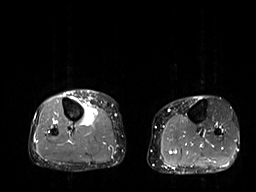
MRI of an extremity soft-tissue mass, one axial slice; slice 17 of 32 in the series (ordered by position); STIR; 6 mm slice thickness; 256 × 192 image matrix, field of view 375 × 281 mm. Female patient. From the clinical record (not read from this slice): histological type: undifferentiated – high grade; grade: high; site of the primary tumour: right thigh.
Structures marked on this image (outlined manually by an expert reader):
- gross tumour volume (mass): bounding box (x1, y1, x2, y2) in pixels: (81, 105, 97, 126)